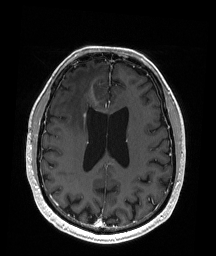
Brain MRI from a brain-tumour surgery series, one axial slice. Position 76 of 192 along the scan axis. T1-weighted post-contrast. 1 mm slice thickness. 216 × 256 image matrix, field of view 211 × 250 mm. From the clinical record (not read from this slice): histopathology: Astrocytoma; WHO grade: 3; IDH mutation: yes; tumour location: Right Frontal.
Outlined on this slice (expert manual segmentation):
- tumour: bounding box [x1, y1, x2, y2] px = [92, 93, 95, 101]